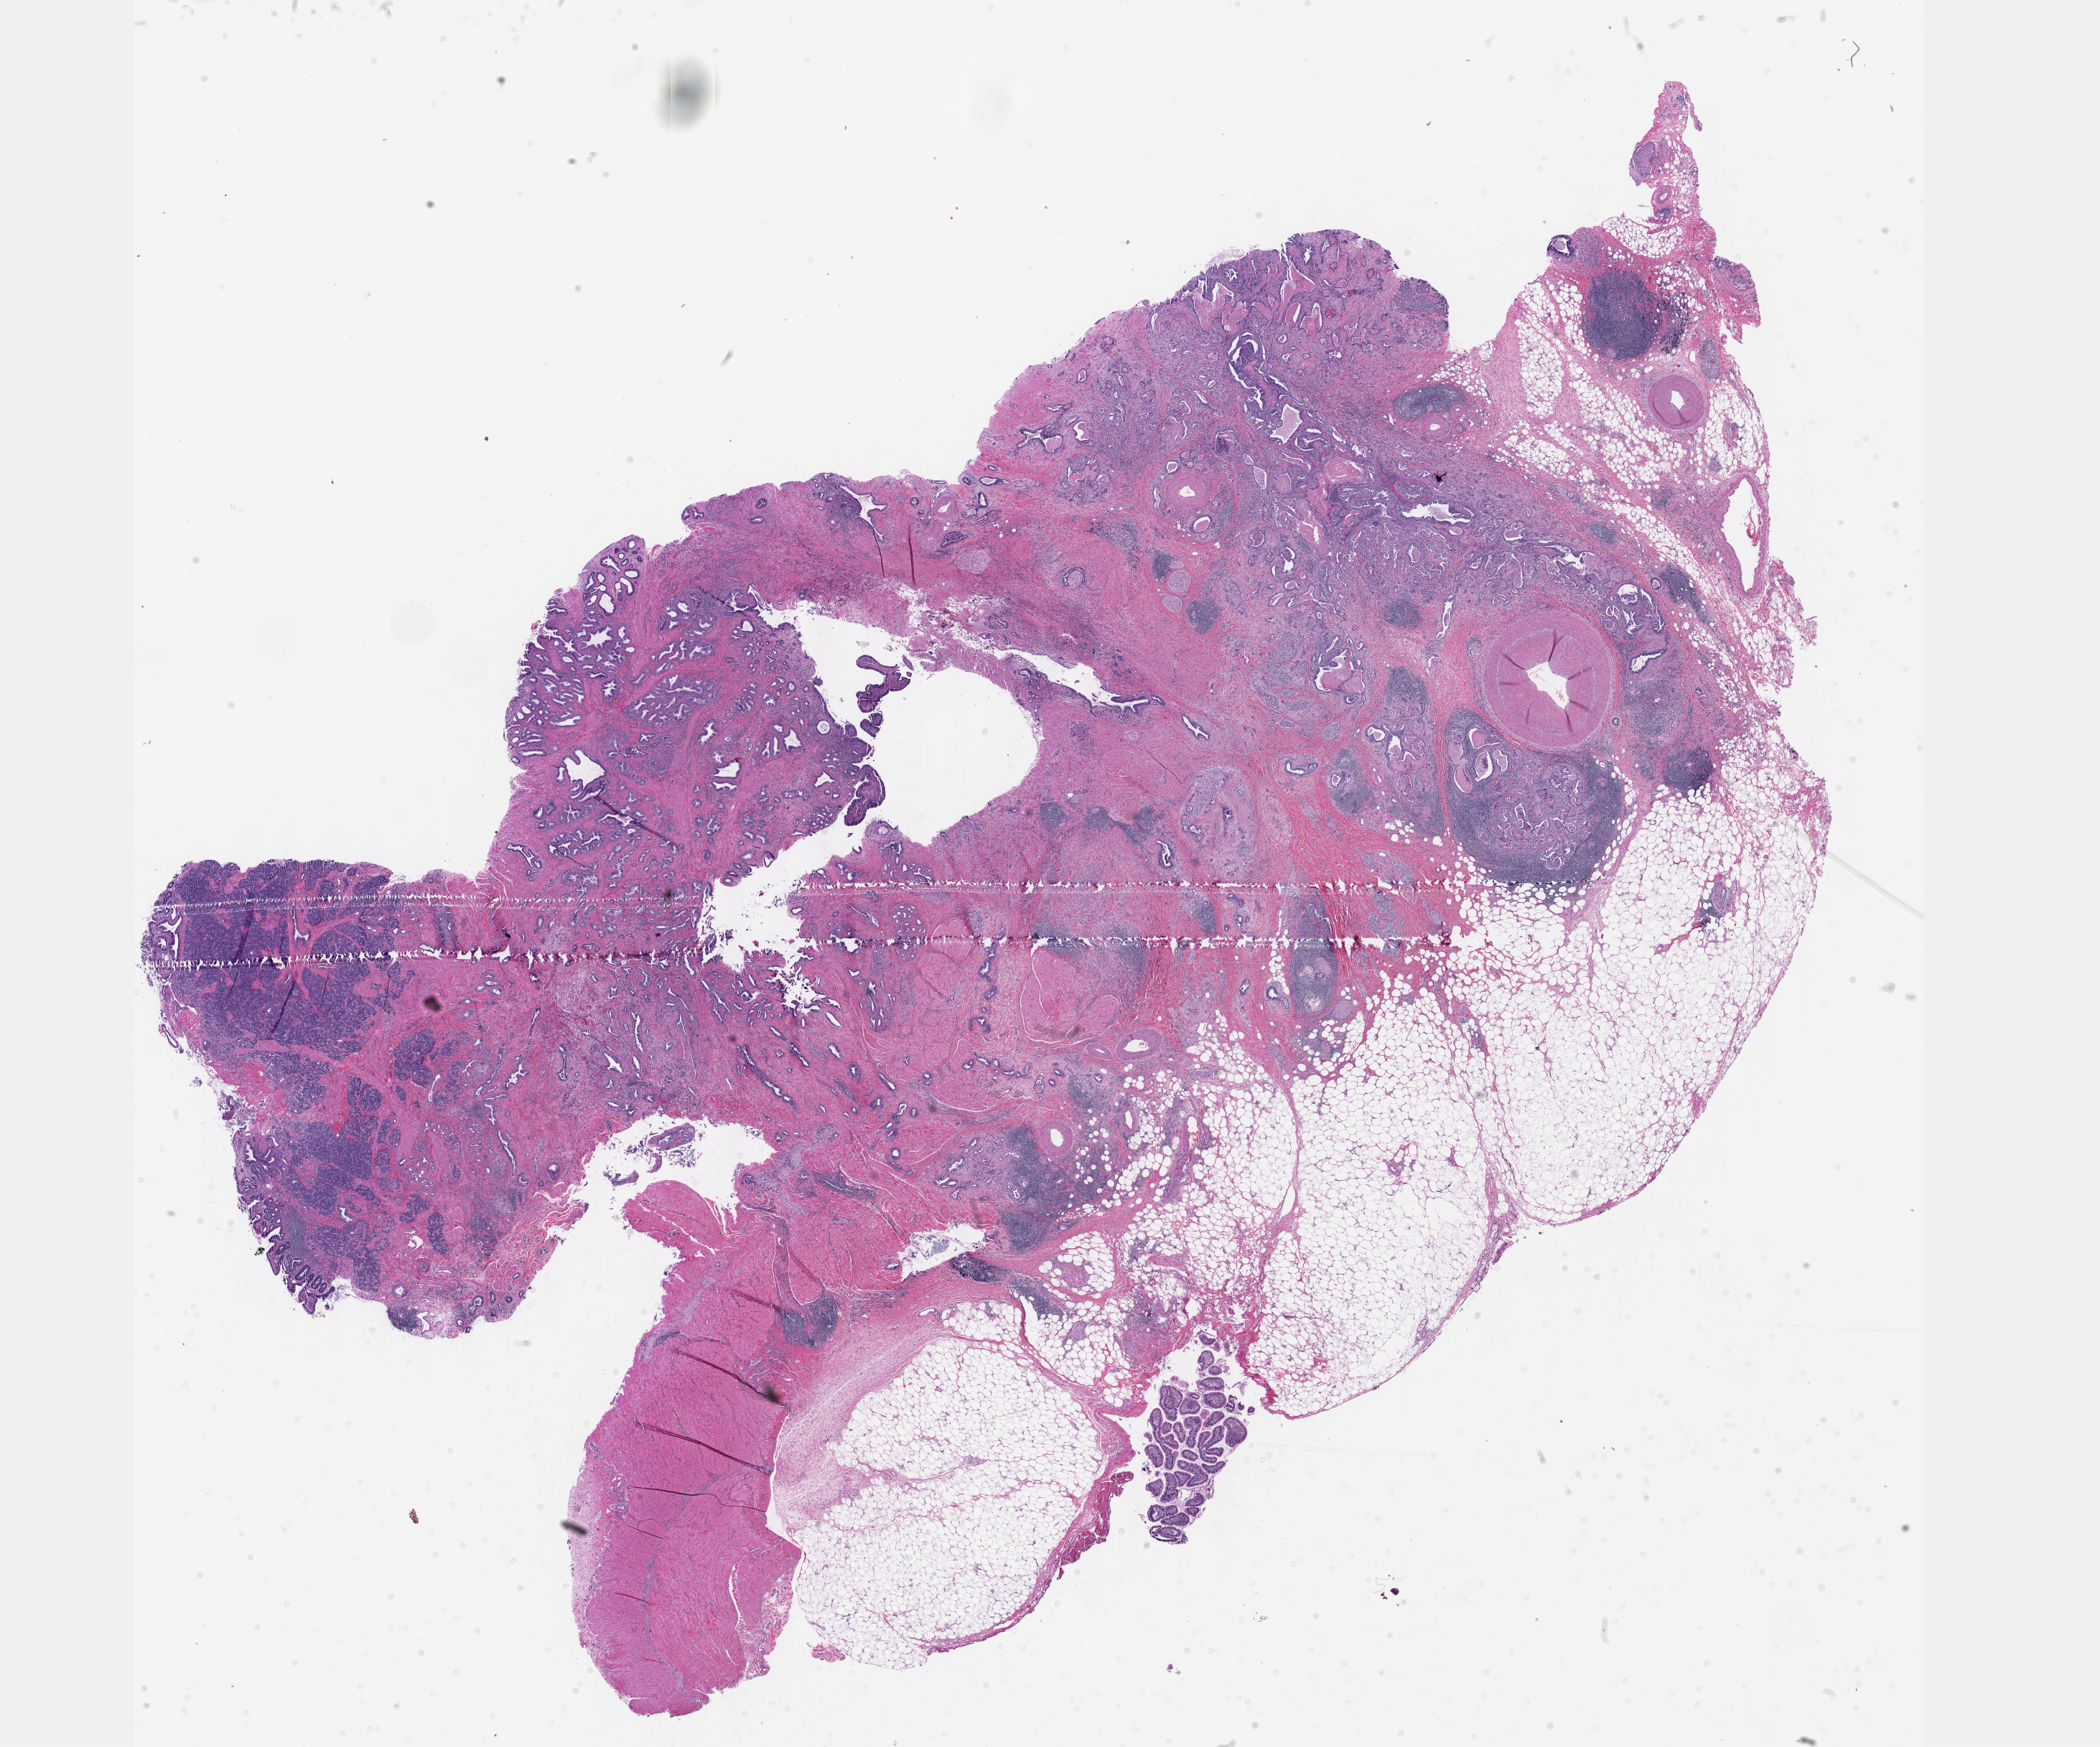
Digitized Hematoxylin and eosin (H&E) stained tissue section (whole slide), whole scanned area (about 23.6 x 19.7 mm) shown as a low-resolution overview; FFPE section; pancreas, primary tumour sample. Female, age 74 years at initial diagnosis. Histologic grade: G2 (moderately differentiated).
* AJCC pathologic stage: IIB
* pathologic diagnosis: Infiltrating duct carcinoma, NOS (head of pancreas)
* lymph nodes positive (case pathology): 7 of 26 examined